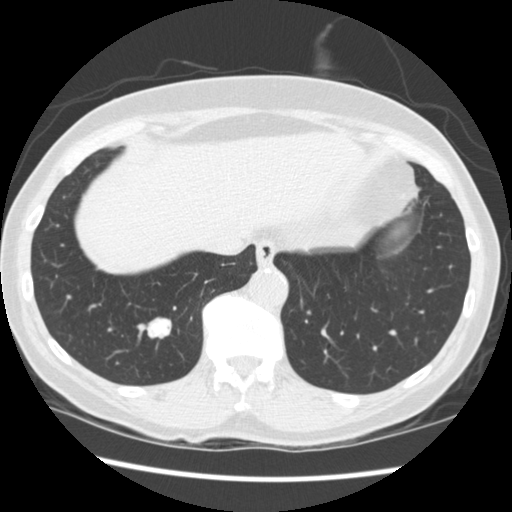
Low-dose screening chest CT, one axial slice. Position 63 of 262 along the scan axis. Reconstruction kernel STANDARD. Lung window (W 1500 / L -600 HU). 2.5 mm slice thickness. 512 × 512 image matrix, field of view 340 × 340 mm.
Annotated regions visible in this slice (outlined manually by an expert reader):
- lesion 1 (tumor, lower lobe of right lung): bounding box [x1, y1, x2, y2] px = [148, 318, 171, 338]